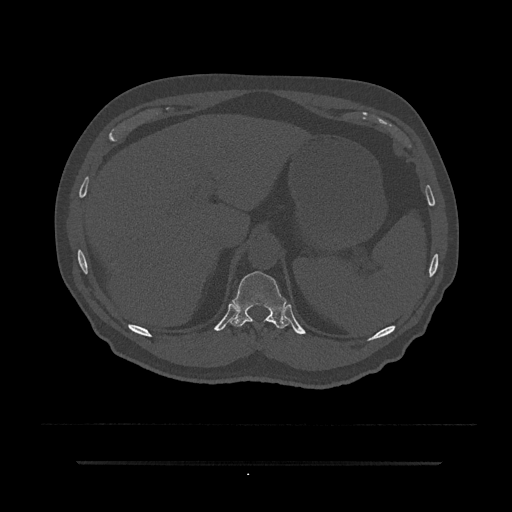
CT including the spine, one axial slice. Position 281 of 797 along the scan axis. Reconstruction kernel Br40s/3. 120 kVp. Bone window (W 1800 / L 400 HU). 0.5 mm slice thickness. 512 × 512 image matrix, field of view 464 × 464 mm. Male patient, age 59 years. Case-level facts recorded for this patient, not image findings: primary cancer: bile ducts; vertebrae with lytic lesions (as recorded): T10.
Outlined on this slice (semi-automatically segmented with operator editing):
- T11 vertebra: bounding box [x1, y1, x2, y2] px = [229, 271, 291, 329]